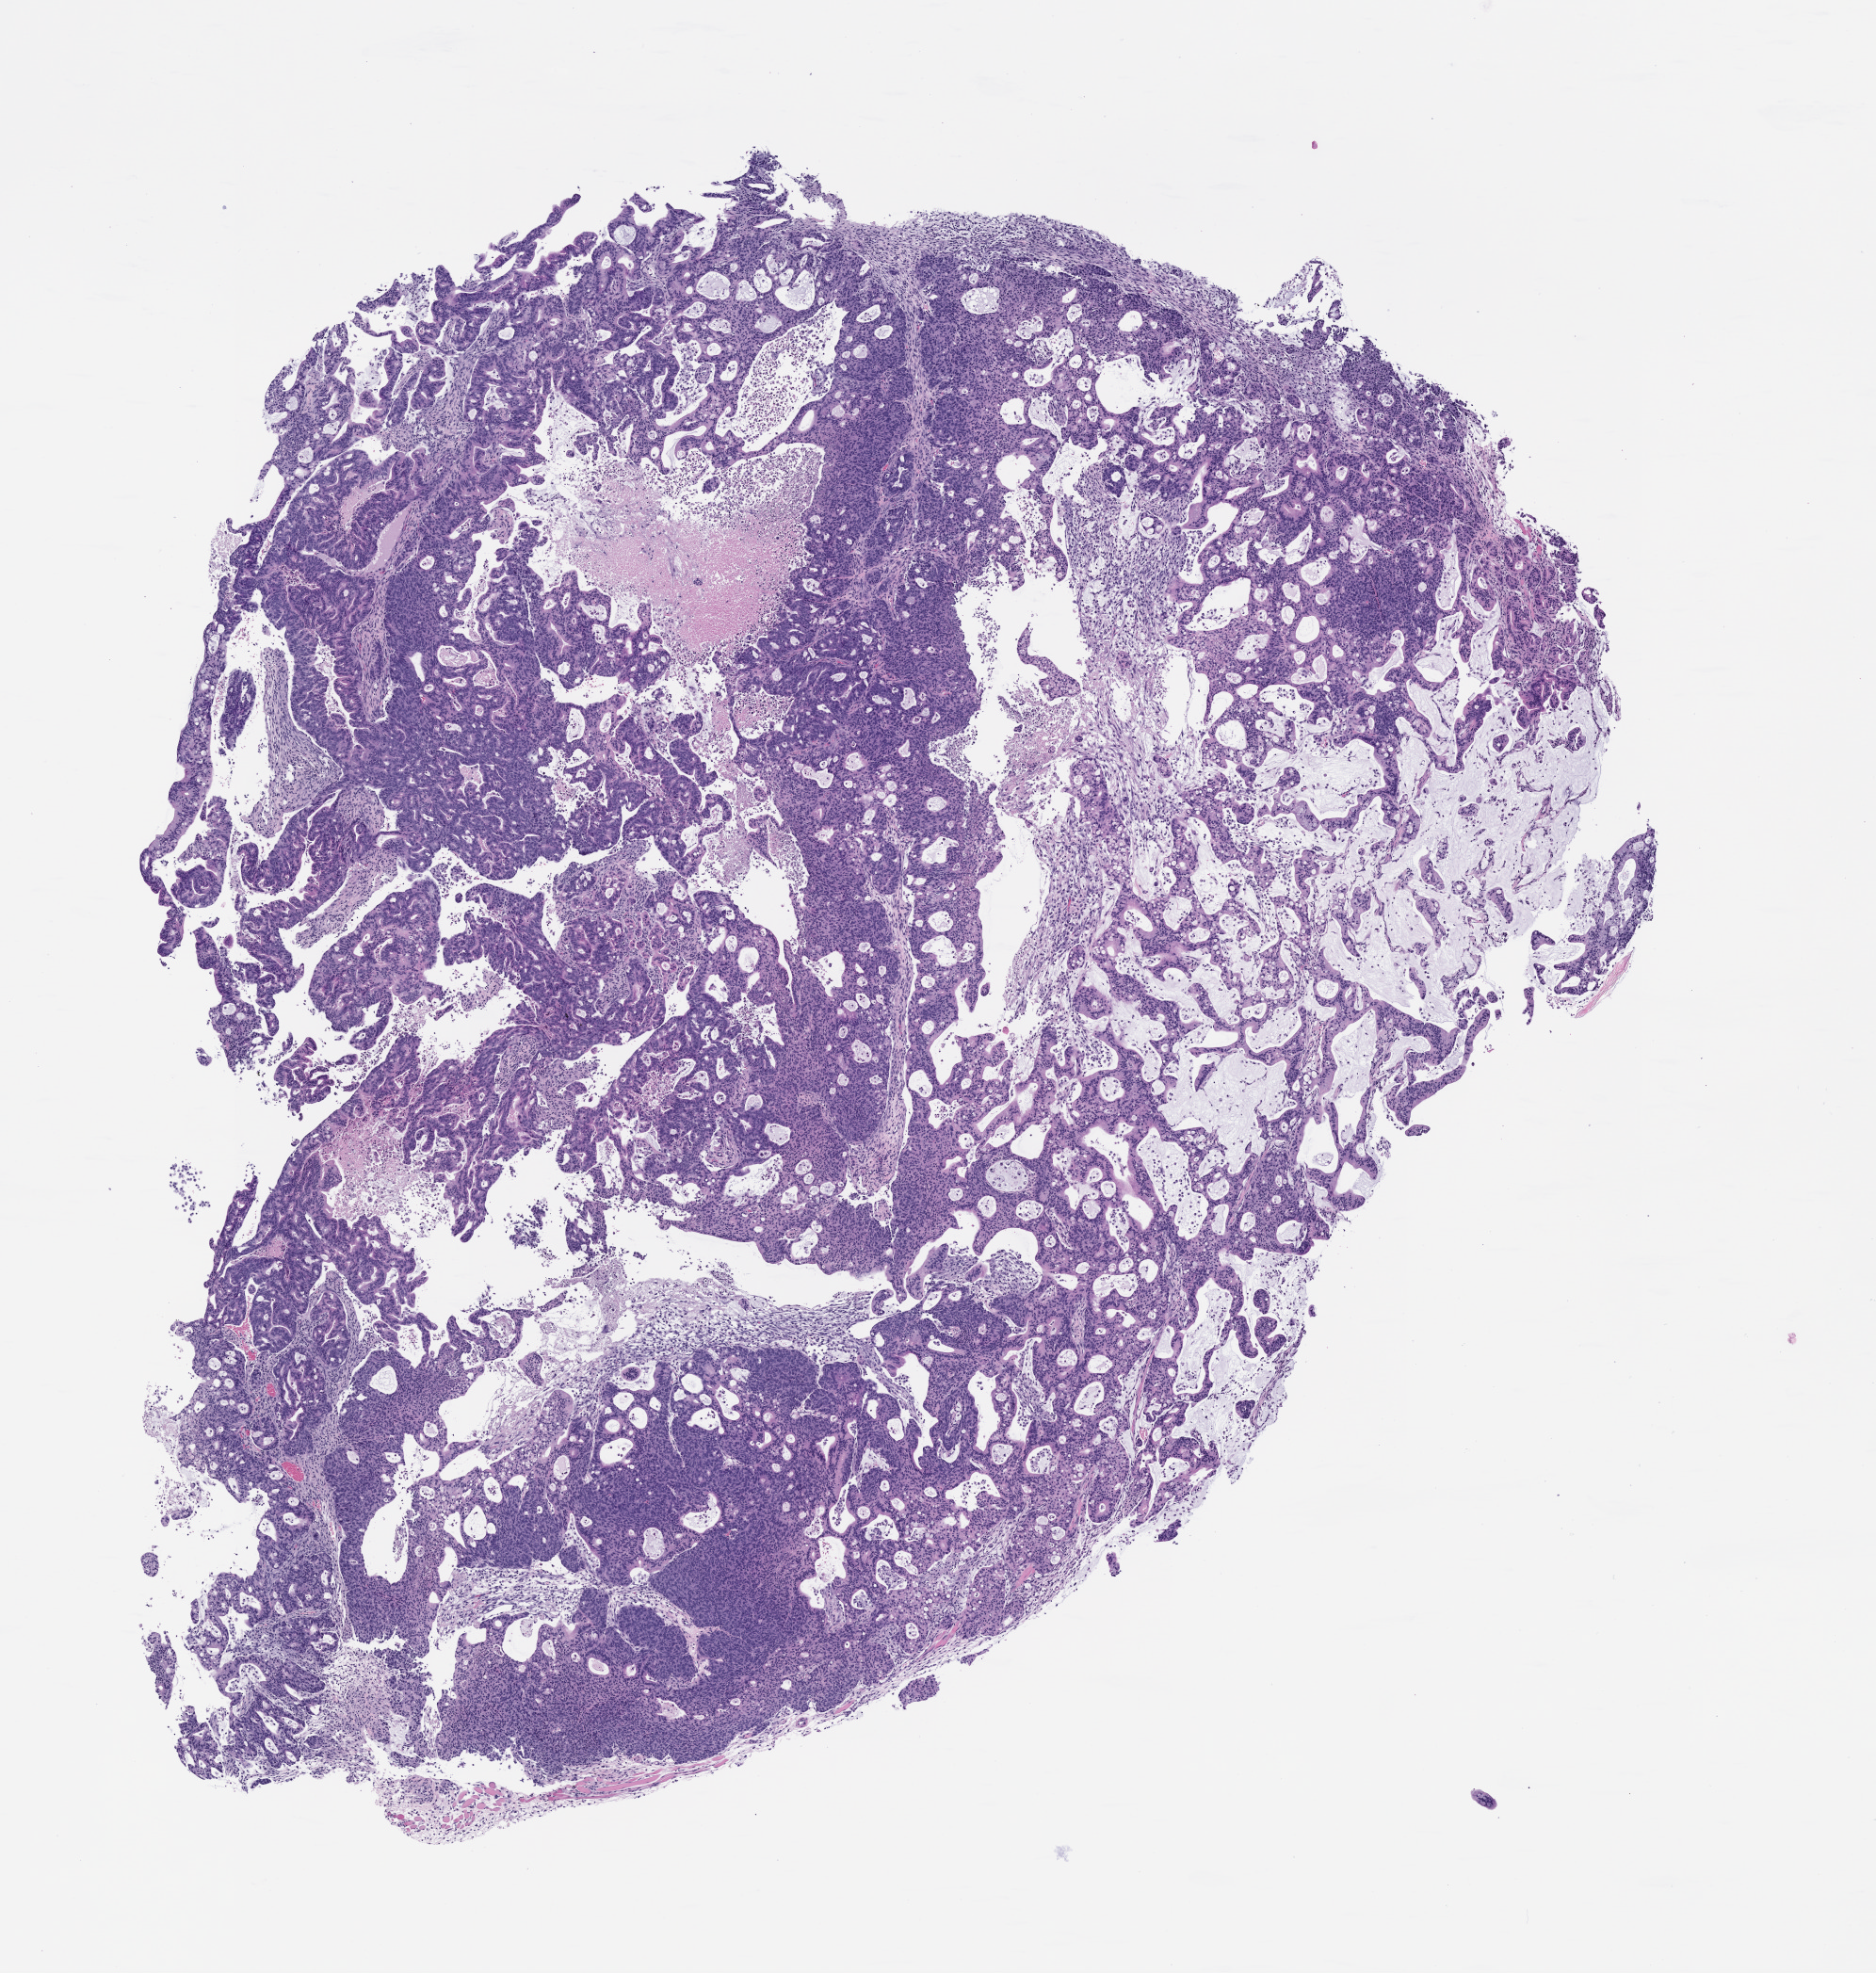
Whole-slide image, H&E: patient-derived xenograft (human tumor grown in a mouse), passage 1, shown as a low-resolution overview of the whole scanned area (about 8.0 x 8.4 mm). Formalin-fixed paraffin-embedded section. Originating tumor site category: colon.
* originating patient diagnosis: Colon Adenocarcinoma